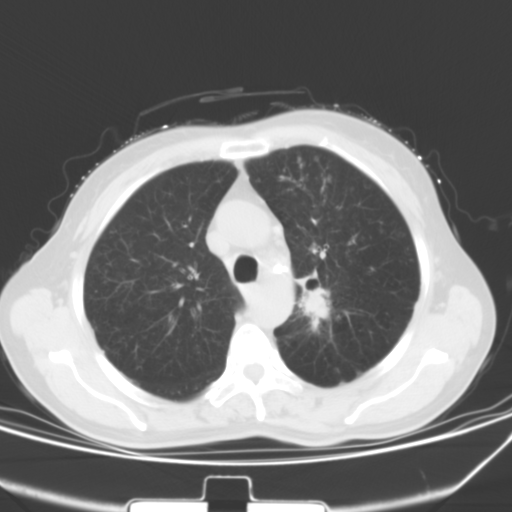
Chest CT, one axial slice; position 41 of 53 along the scan axis; lung window (W 1500 / L -600 HU); 5 mm slice thickness; 512 × 512 image matrix. Patient: female, 60 years. From the clinical record (not read from this slice): clinical TNM (as recorded): T1b N0 M0.
Annotated regions visible in this slice (bounding box drawn by a radiologist):
- lung tumour (recorded histology: squamous cell carcinoma): box from (x=303, y=277) to (x=344, y=325) px